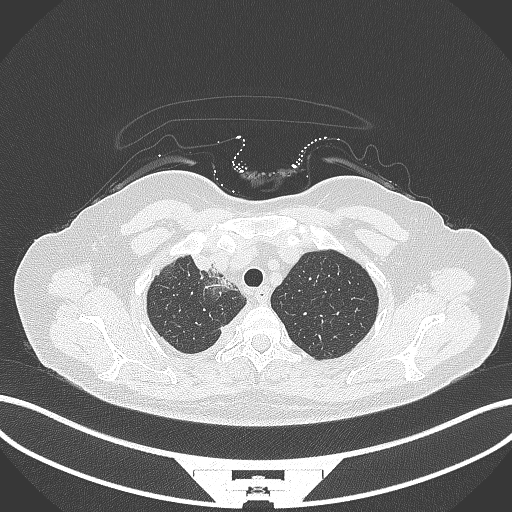
Chest CT, one axial slice; position 264 of 305 along the scan axis; reconstruction kernel B70f; lung window (W 1500 / L -600 HU); 1 mm slice thickness; 512 × 512 image matrix, field of view 400 × 400 mm. Patient: female, 52 years. From the clinical record (not read from this slice): clinical TNM (as recorded): T3 N1 M1.
Structures marked on this image (rectangle marked by the reading radiologist):
- lung tumour (recorded histology: adenocarcinoma): box from (x=191, y=252) to (x=221, y=282) px